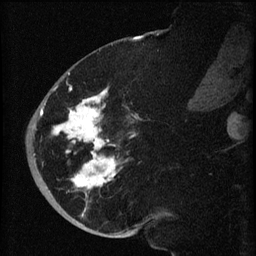
Breast MRI (dynamic contrast-enhanced), one sagittal slice; slice 25 of 60 in the series (ordered by position); dynamic contrast-enhanced series, image 2 of 3 at this slice position (ordered by acquisition); 1.5 T; TE 4.2 ms, TR 8.2 ms; 2 mm slice thickness; 256 × 256 image matrix. Female patient, age 71 years.
Structures marked on this image (semi-automatically segmented with operator editing):
- analysis volume of interest (the breast-tissue region the enhancement analysis was run in; not a lesion): box from (x=40, y=72) to (x=139, y=196) px
- tumour enhancement mask (voxels above the 70 % enhancement threshold inside the analysis volume of interest): (x=40, y=73)–(x=136, y=190)